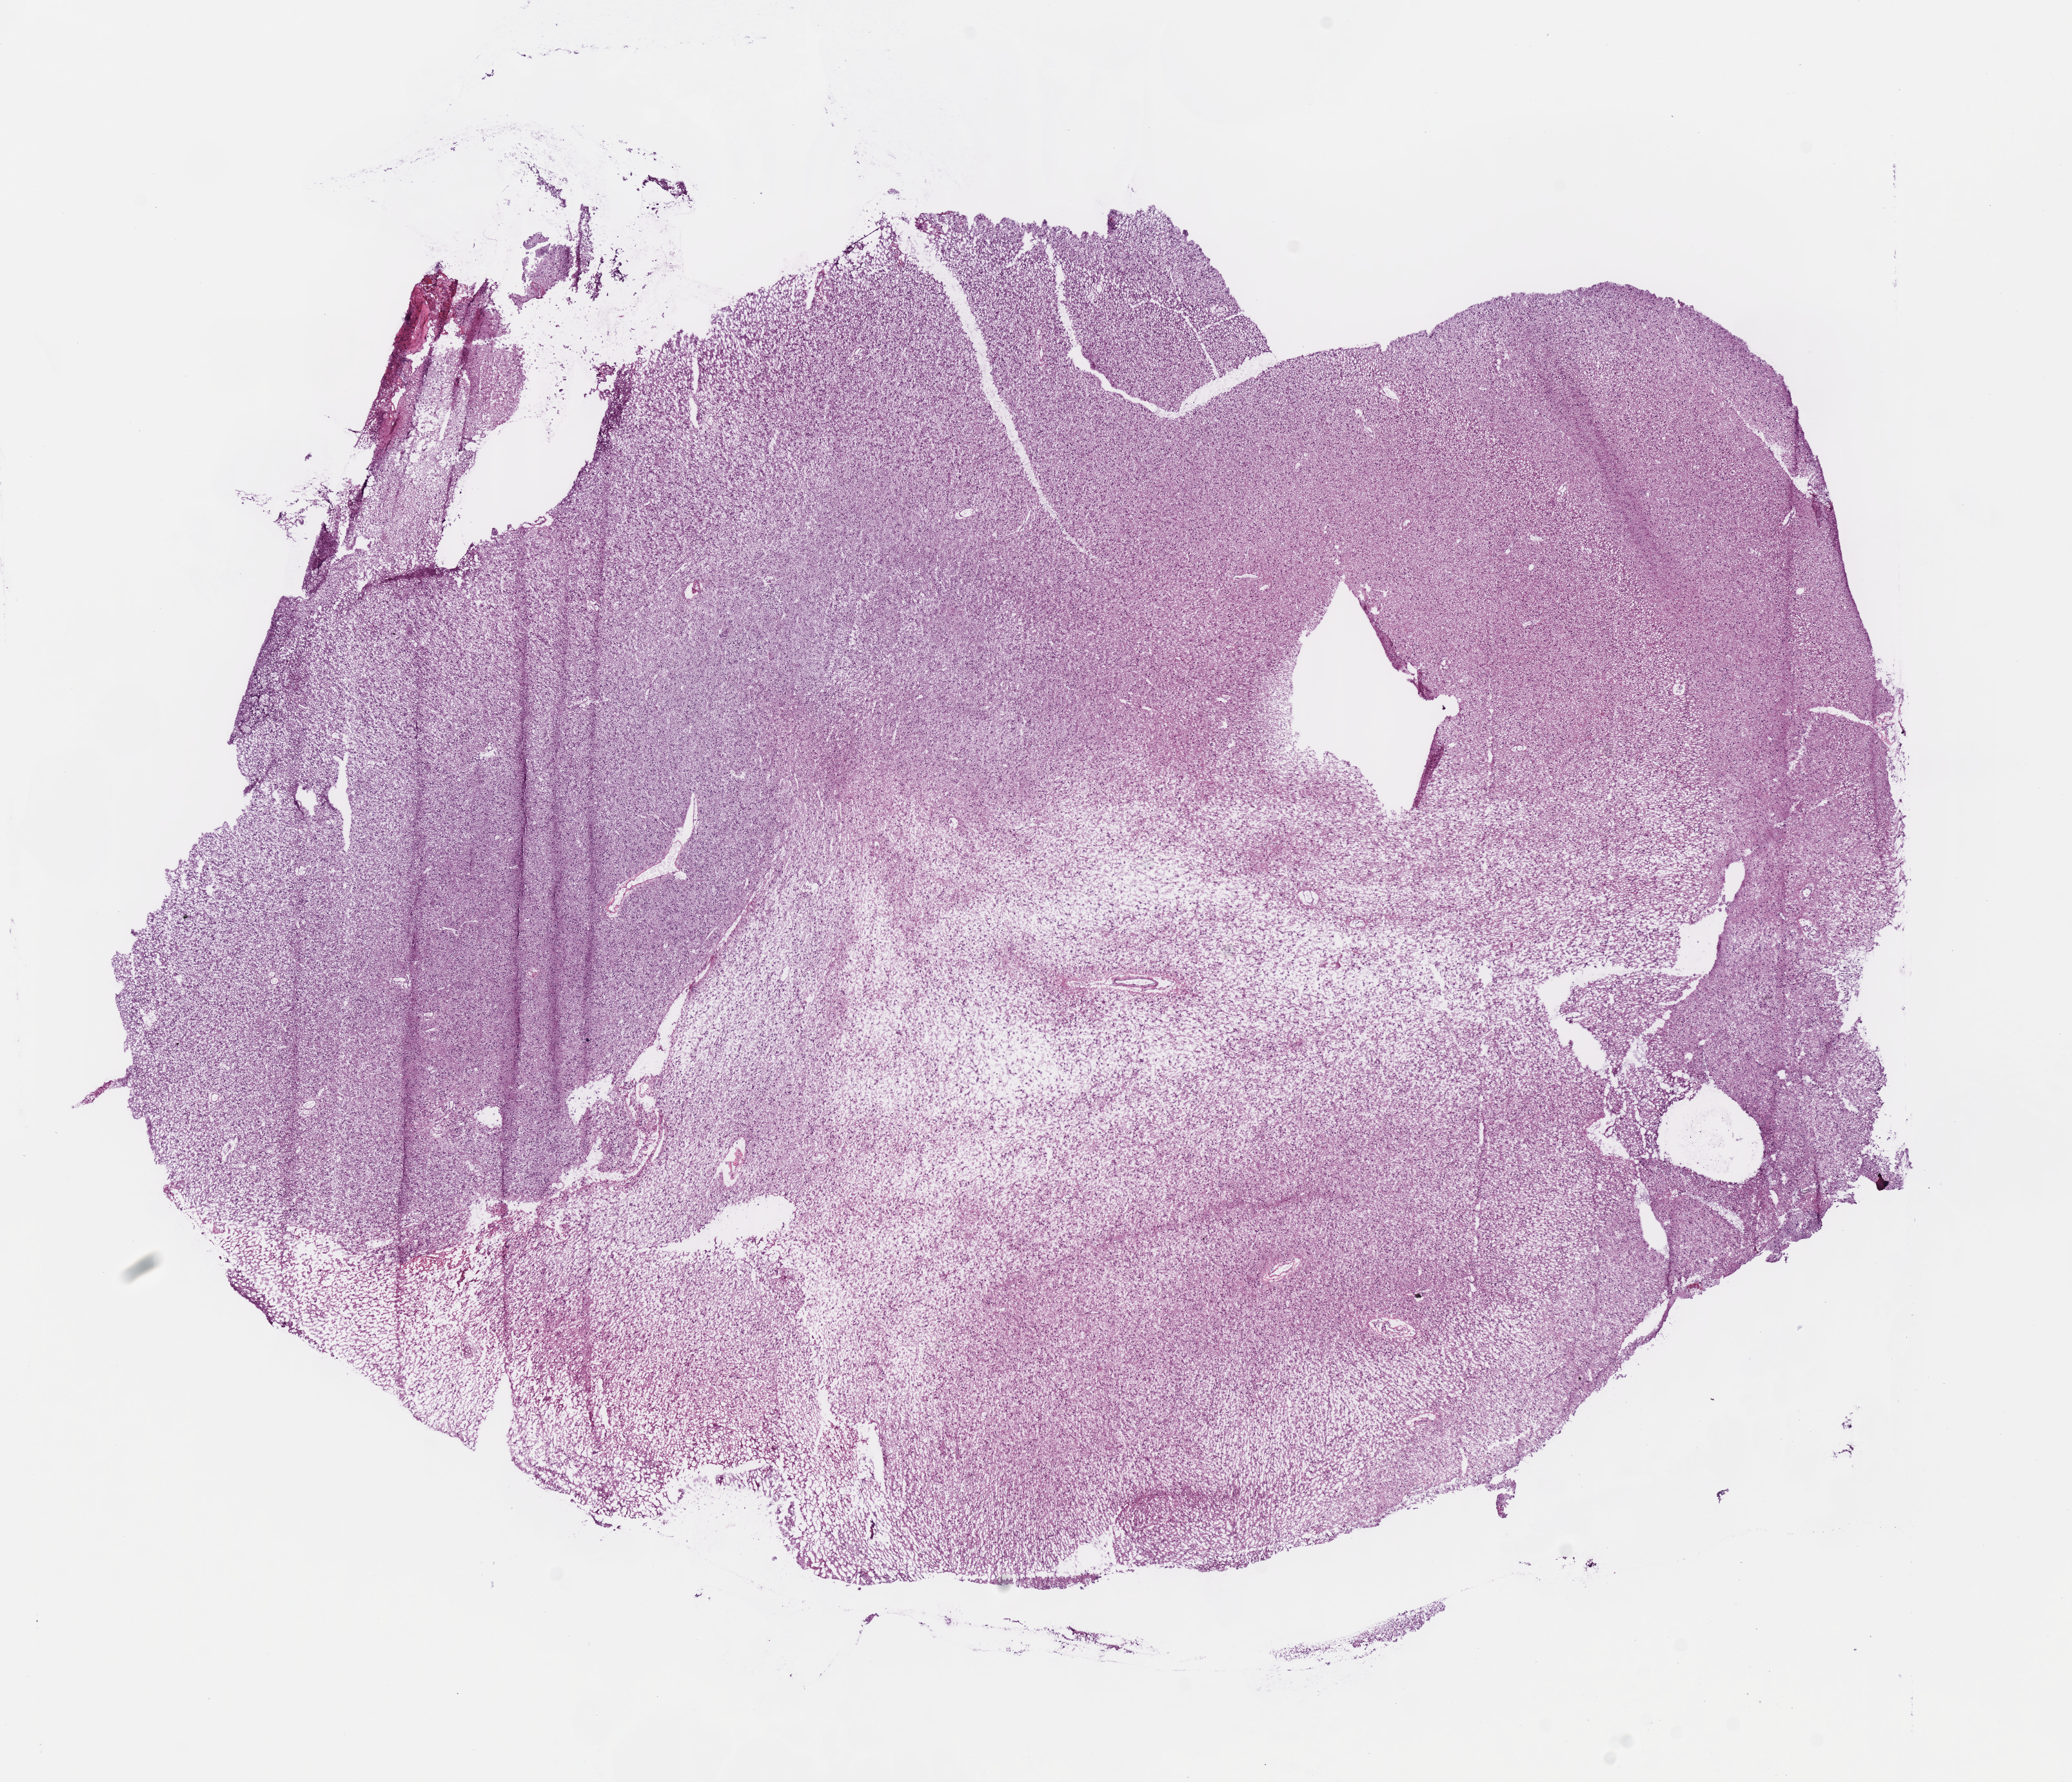
Whole-slide histology image, H&E-stained, low-resolution overview of the scanned area, about 12.7 x 10.9 mm (slide scanned at 40x), frozen section from the bottom of the tissue portion, brain, primary tumour sample. Patient: male, age at initial diagnosis 61 years. Histologic grade: G2 (moderately differentiated). Slide review estimates, as recorded: tumour cells 100%, tumour nuclei 75%, normal cells 0%, stromal cells 0%, necrosis 0%.
* pathologic diagnosis: Mixed glioma (cerebrum)
* laterality: right